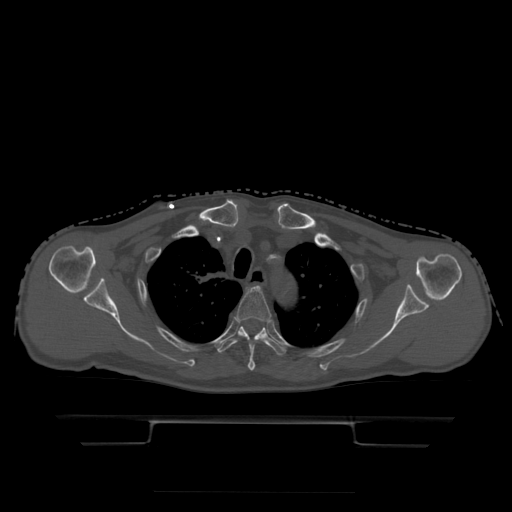
CT including the spine, one axial slice; position 364 of 522 along the scan axis; bone window (W 1800 / L 400 HU); 512 × 512 image matrix, field of view 436 × 436 mm. Patient age 68 years. From the clinical record (not read from this slice): primary cancer: urothelial.
Outlined on this slice (semi-automatically segmented with operator editing):
- T3 vertebra: bounding box (x1, y1, x2, y2) in pixels: (236, 288, 272, 371)
- T4 vertebra: (217, 326, 286, 356)